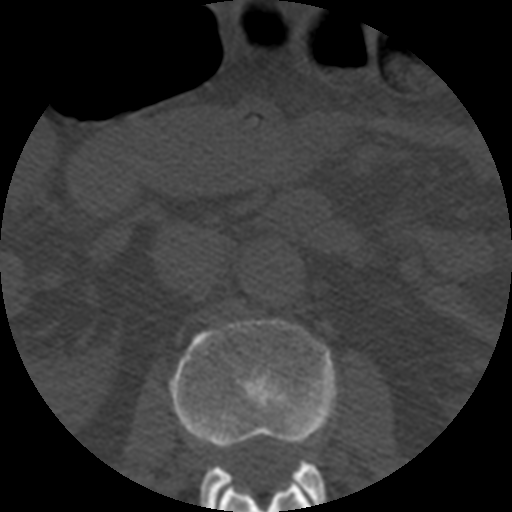
CT including the spine, one axial slice. Slice 166 of 508 in the series (ordered by position). Reconstruction kernel STANDARD. 120 kVp. Bone window (W 1800 / L 400 HU). 512 × 512 image matrix, field of view 160 × 160 mm. Patient age 57 years. Case-level facts recorded for this patient, not image findings: primary cancer: prostate.
Outlined on this slice (semi-automatic segmentation, software-assisted and operator-edited):
- L1 vertebra: box from (x=219, y=481) to (x=312, y=512) px
- L2 vertebra: (x=170, y=319)–(x=336, y=512)